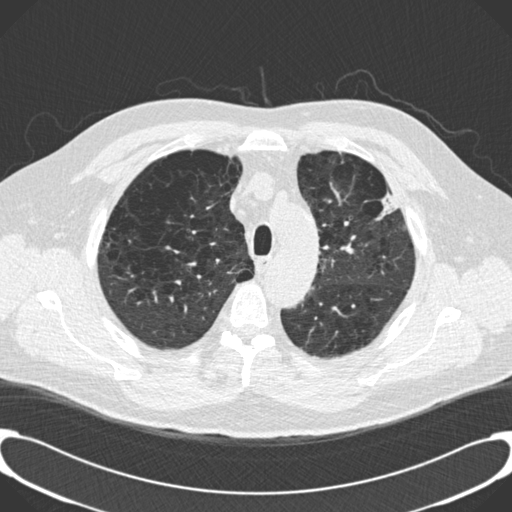
Low-dose screening chest CT, one axial slice; position 153 of 189 along the scan axis; lung window (W 1500 / L -600 HU); 2 mm slice thickness; 512 × 512 image matrix.
Outlined on this slice (expert manual segmentation):
- lesion 1 (tumor, upper lobe of left lung): bounding box <377,192,400,220> (left, top, right, bottom; pixels)